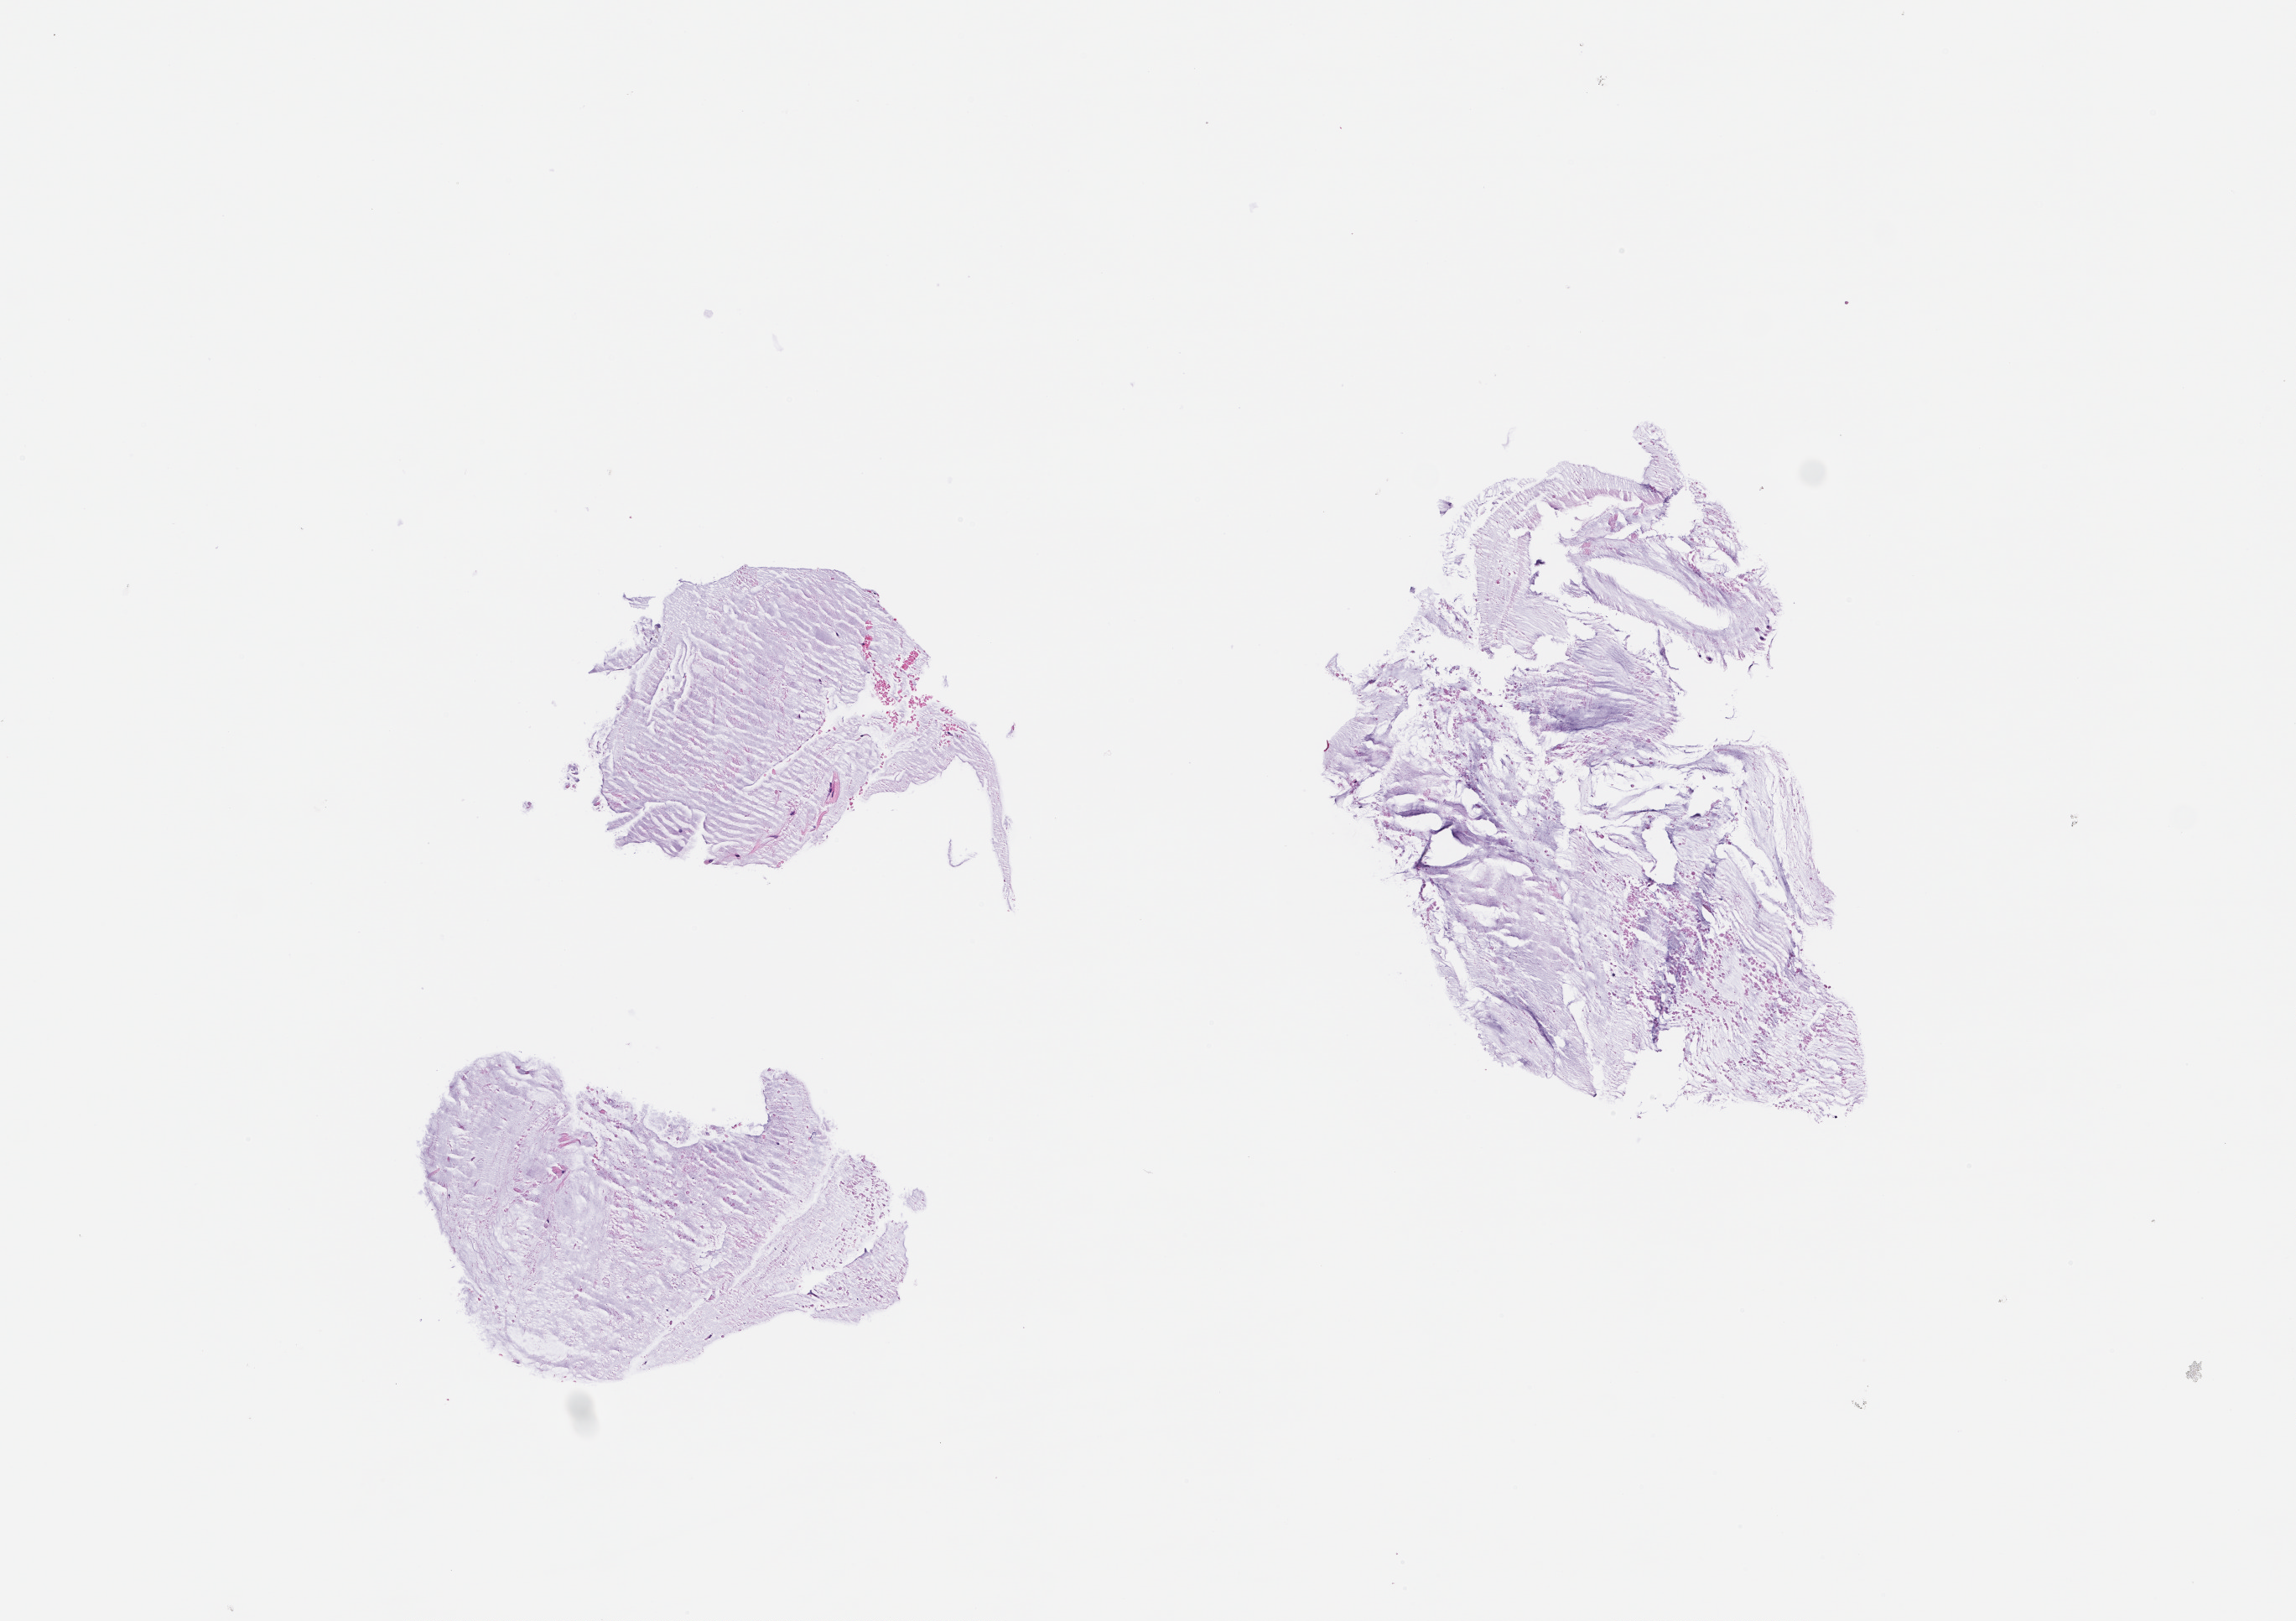
Haematoxylin and eosin whole-slide image — whole scanned area (about 5.5 x 3.9 mm) shown as a low-resolution overview, FFPE section. Male patient.
• this section: metastasis (sampled organ not recorded)
• patient diagnosis (primary): Colorectal Carcinoma